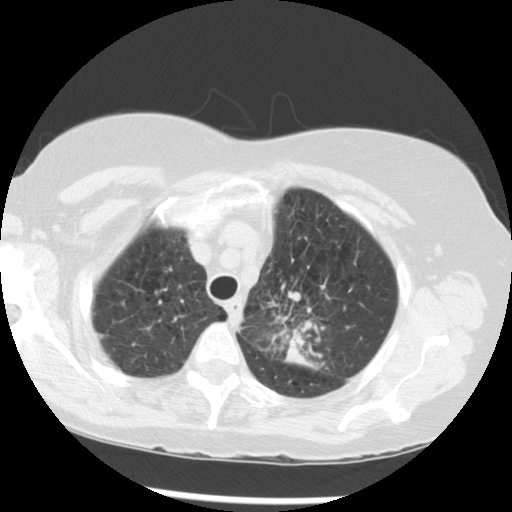
Low-dose screening chest CT, one axial slice. Position 231 of 283 along the scan axis. Reconstruction kernel STANDARD. 120 kVp. Lung window (W 1500 / L -600 HU). 2.5 mm slice thickness. 512 × 512 image matrix.
Annotated regions visible in this slice (expert manual segmentation):
- lesion 1 (tumor, upper lobe of left lung): bounding box <284,291,320,371> (left, top, right, bottom; pixels)